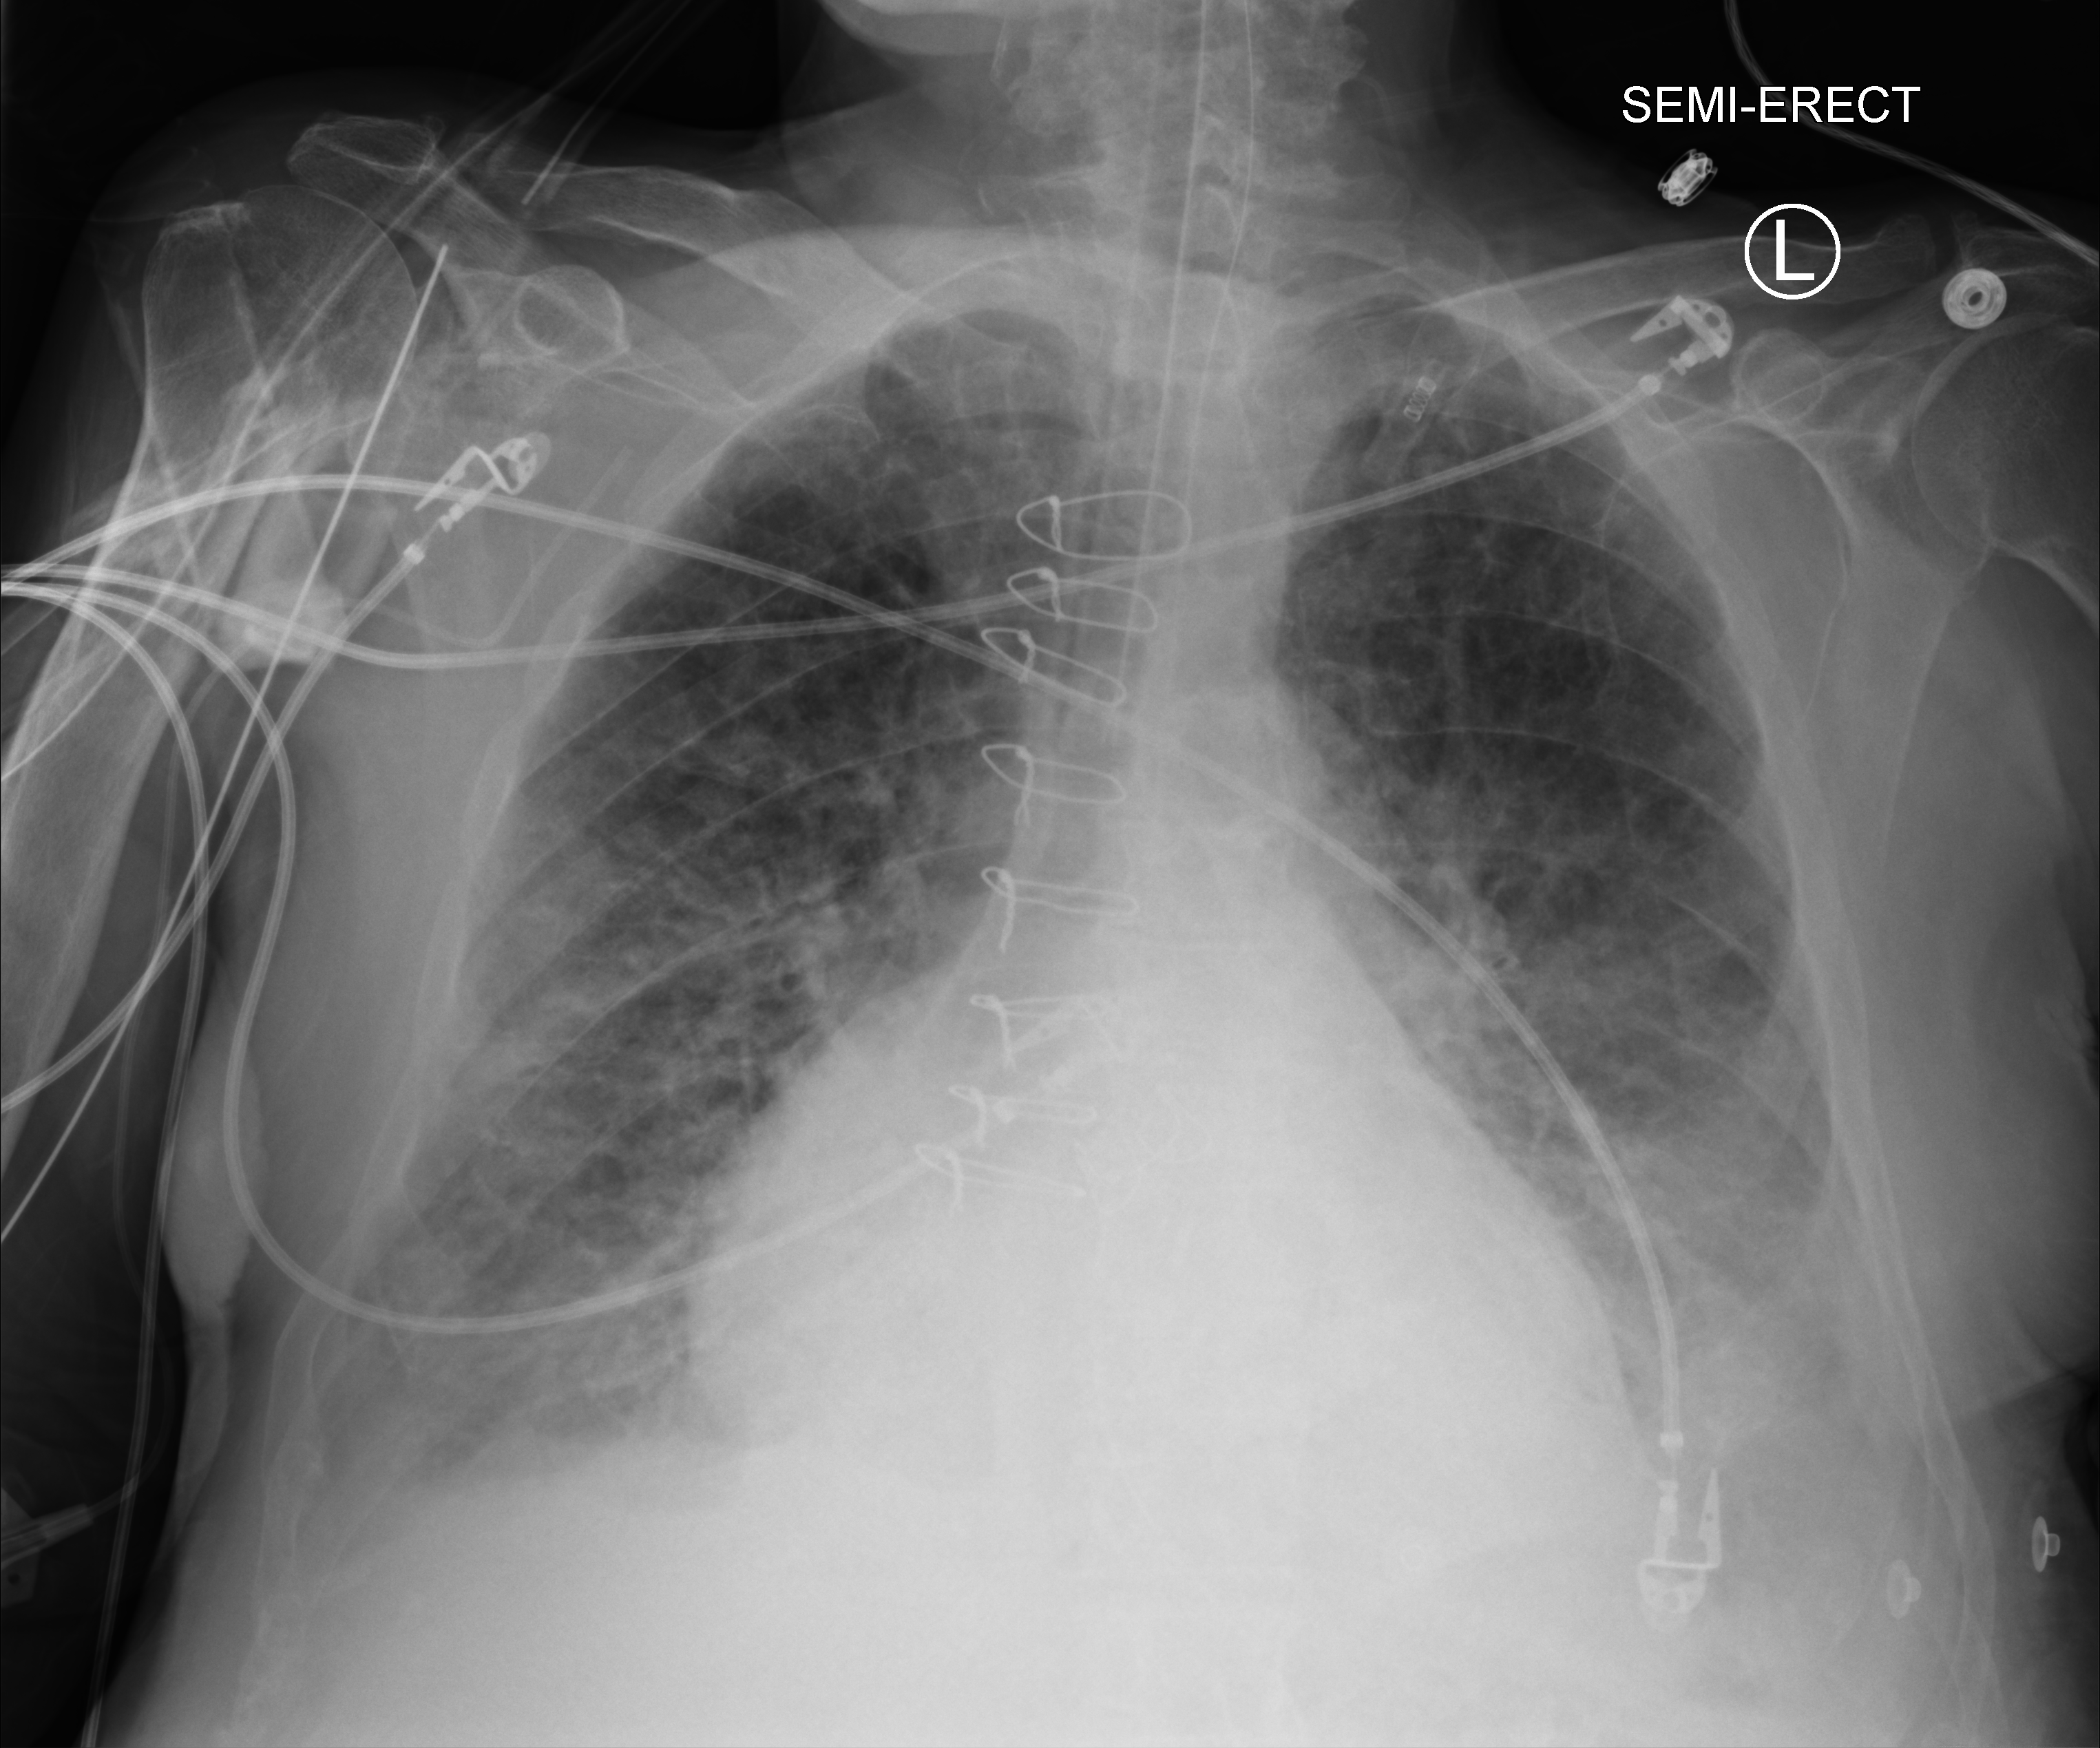
Chest X-ray (portable), anteroposterior (AP) projection. Male patient hospitalised with COVID-19, age 75–90 years.
From the hospital-stay record, not from the radiograph (when in the stay this image was taken is not recorded): admitted to intensive care during this hospital stay: yes; mechanically ventilated during this hospital stay: yes.